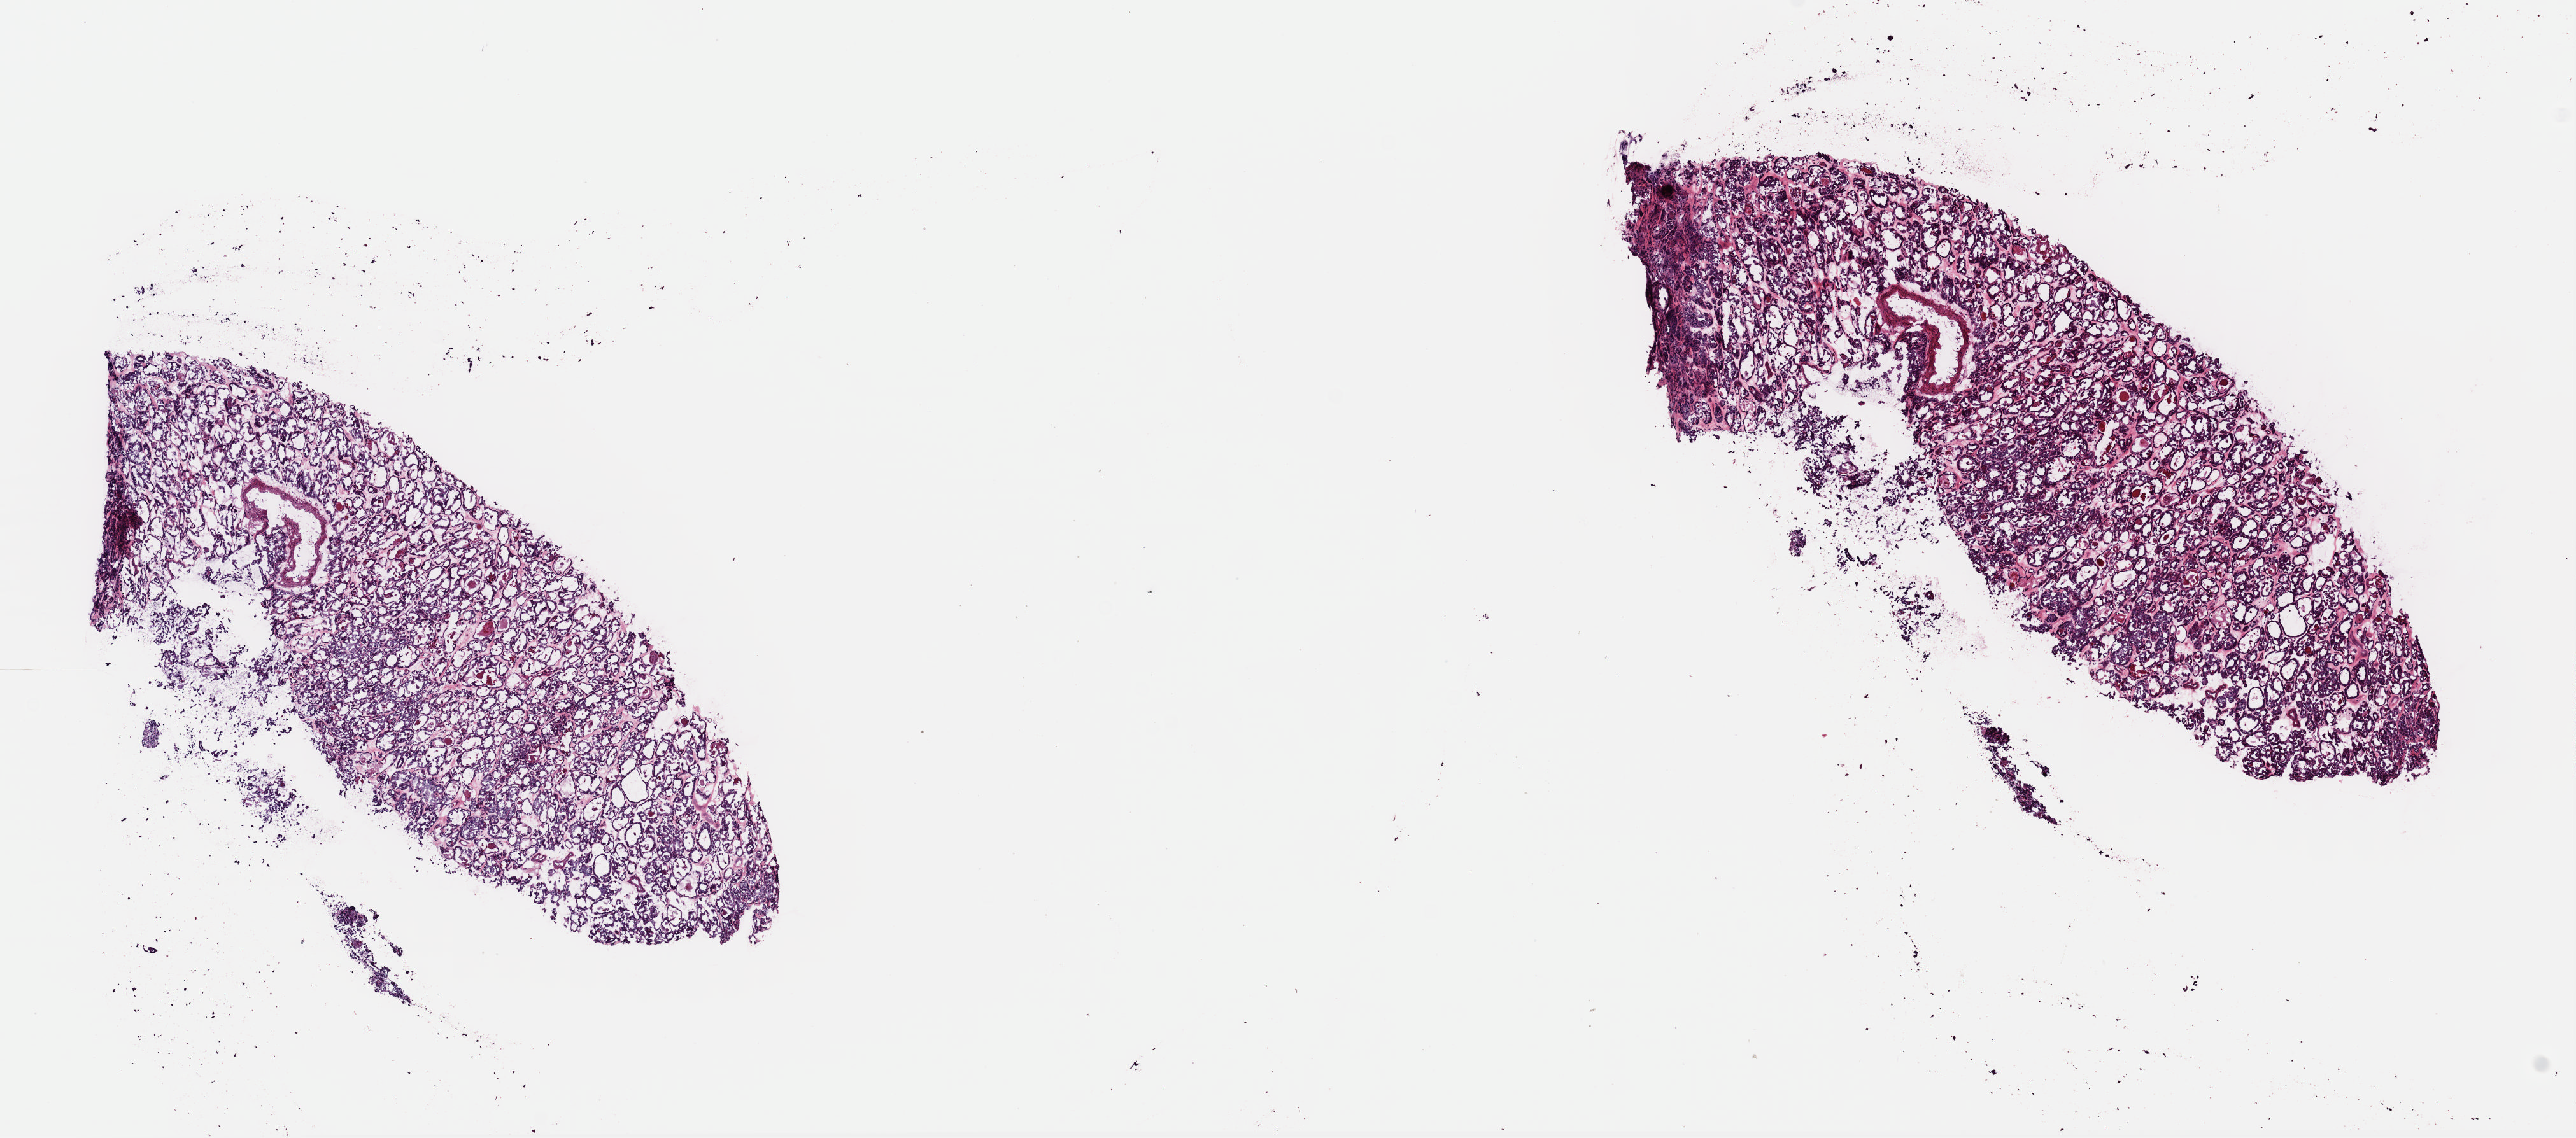
Digitized Hematoxylin and eosin (H&E) stained tissue section (whole slide) — a low-resolution overview of the entire scanned area, about 16.0 x 7.1 mm (acquisition: 40x scan). Frozen section from the top of the tissue portion. Sample: primary tumour, thyroid. Patient: female, age at initial diagnosis 77 years. Slide review estimates, as recorded: tumour cells 90%, tumour nuclei 90%, normal cells 0%, stromal cells 10%, necrosis 0%. Inflammatory infiltration, as recorded: lymphocyte infiltration 0%, monocyte infiltration 0%, neutrophil infiltration 0%.
Laterality: right. AJCC pathologic stage: II (7th edition). Pathologic diagnosis: Papillary carcinoma, follicular variant (thyroid gland).